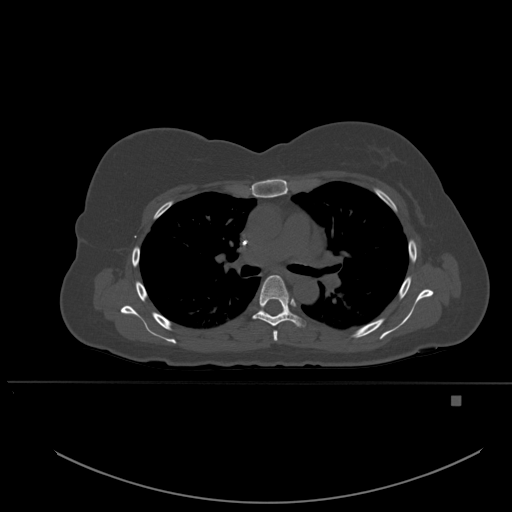
CT including the spine, one axial slice. Slice 366 of 651 in the series (ordered by position). Bone window (W 1800 / L 400 HU). 1.5 mm slice thickness. 512 × 512 image matrix. Patient: female, 49 years. Case-level facts recorded for this patient, not image findings: primary cancer: breast.
Annotated regions visible in this slice (semi-automatically segmented with operator editing):
- T4 vertebra: bounding box [x1, y1, x2, y2] px = [273, 330, 278, 341]
- T5 vertebra: [253, 275, 305, 327]